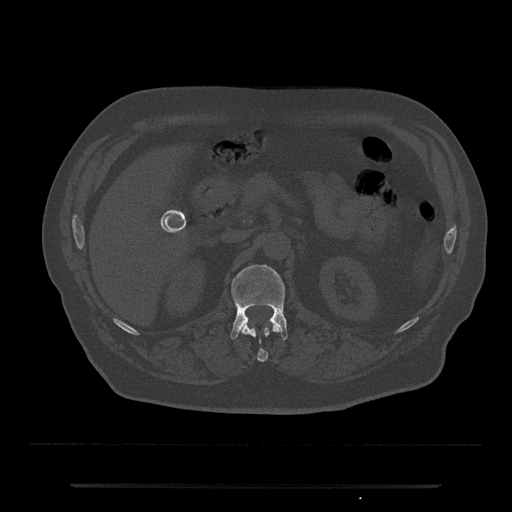
CT including the spine, one axial slice. Slice 555 of 797 in the series (ordered by position). Reconstruction kernel Br40s/3. 120 kVp. Bone window (W 1800 / L 400 HU). 0.5 mm slice thickness. 512 × 512 image matrix. Male patient, age 80 years. From the clinical record (not read from this slice): primary cancer: prostate.
Outlined on this slice (semi-automatic segmentation, software-assisted and operator-edited):
- L1 vertebra: bounding box [x1, y1, x2, y2] px = [230, 265, 288, 340]
- T12 vertebra: [242, 324, 280, 362]